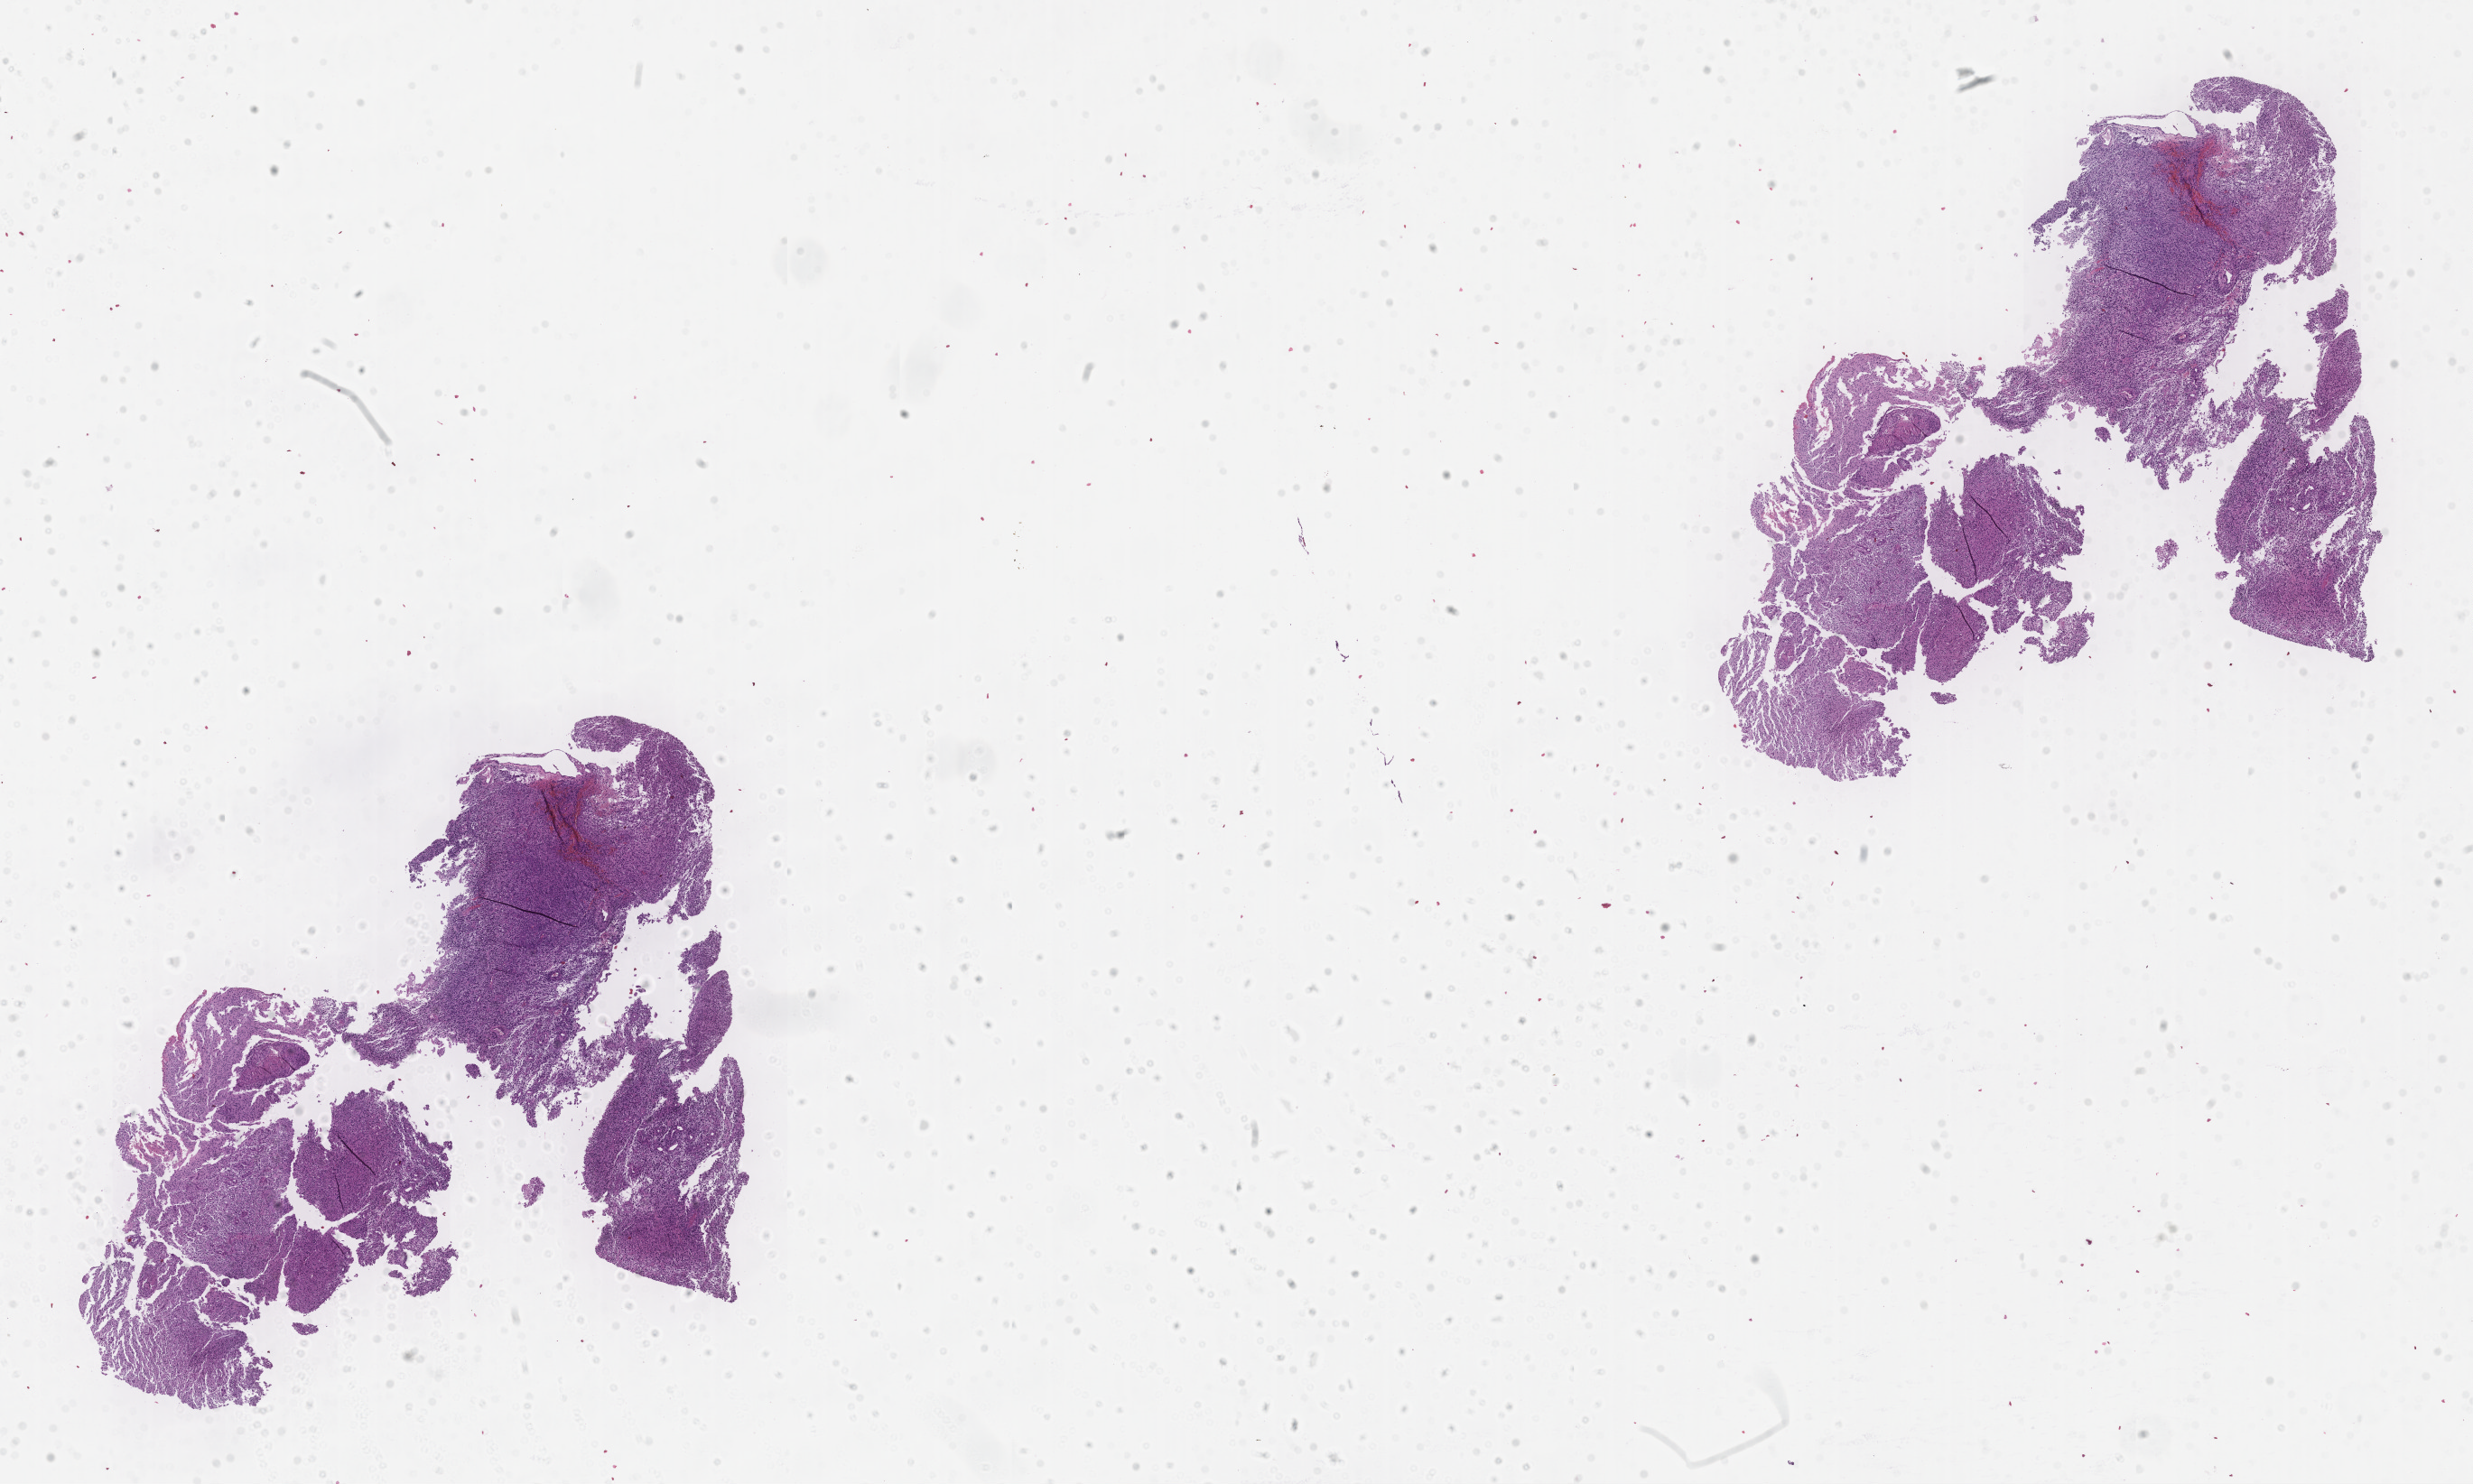
Digitized H&E-stained tissue section (whole slide), a low-resolution overview of the entire scanned area, about 22.1 x 13.2 mm. Tumour tissue sample, brain. Patient: female, age 51 years.
Diagnosis: Glioblastoma.